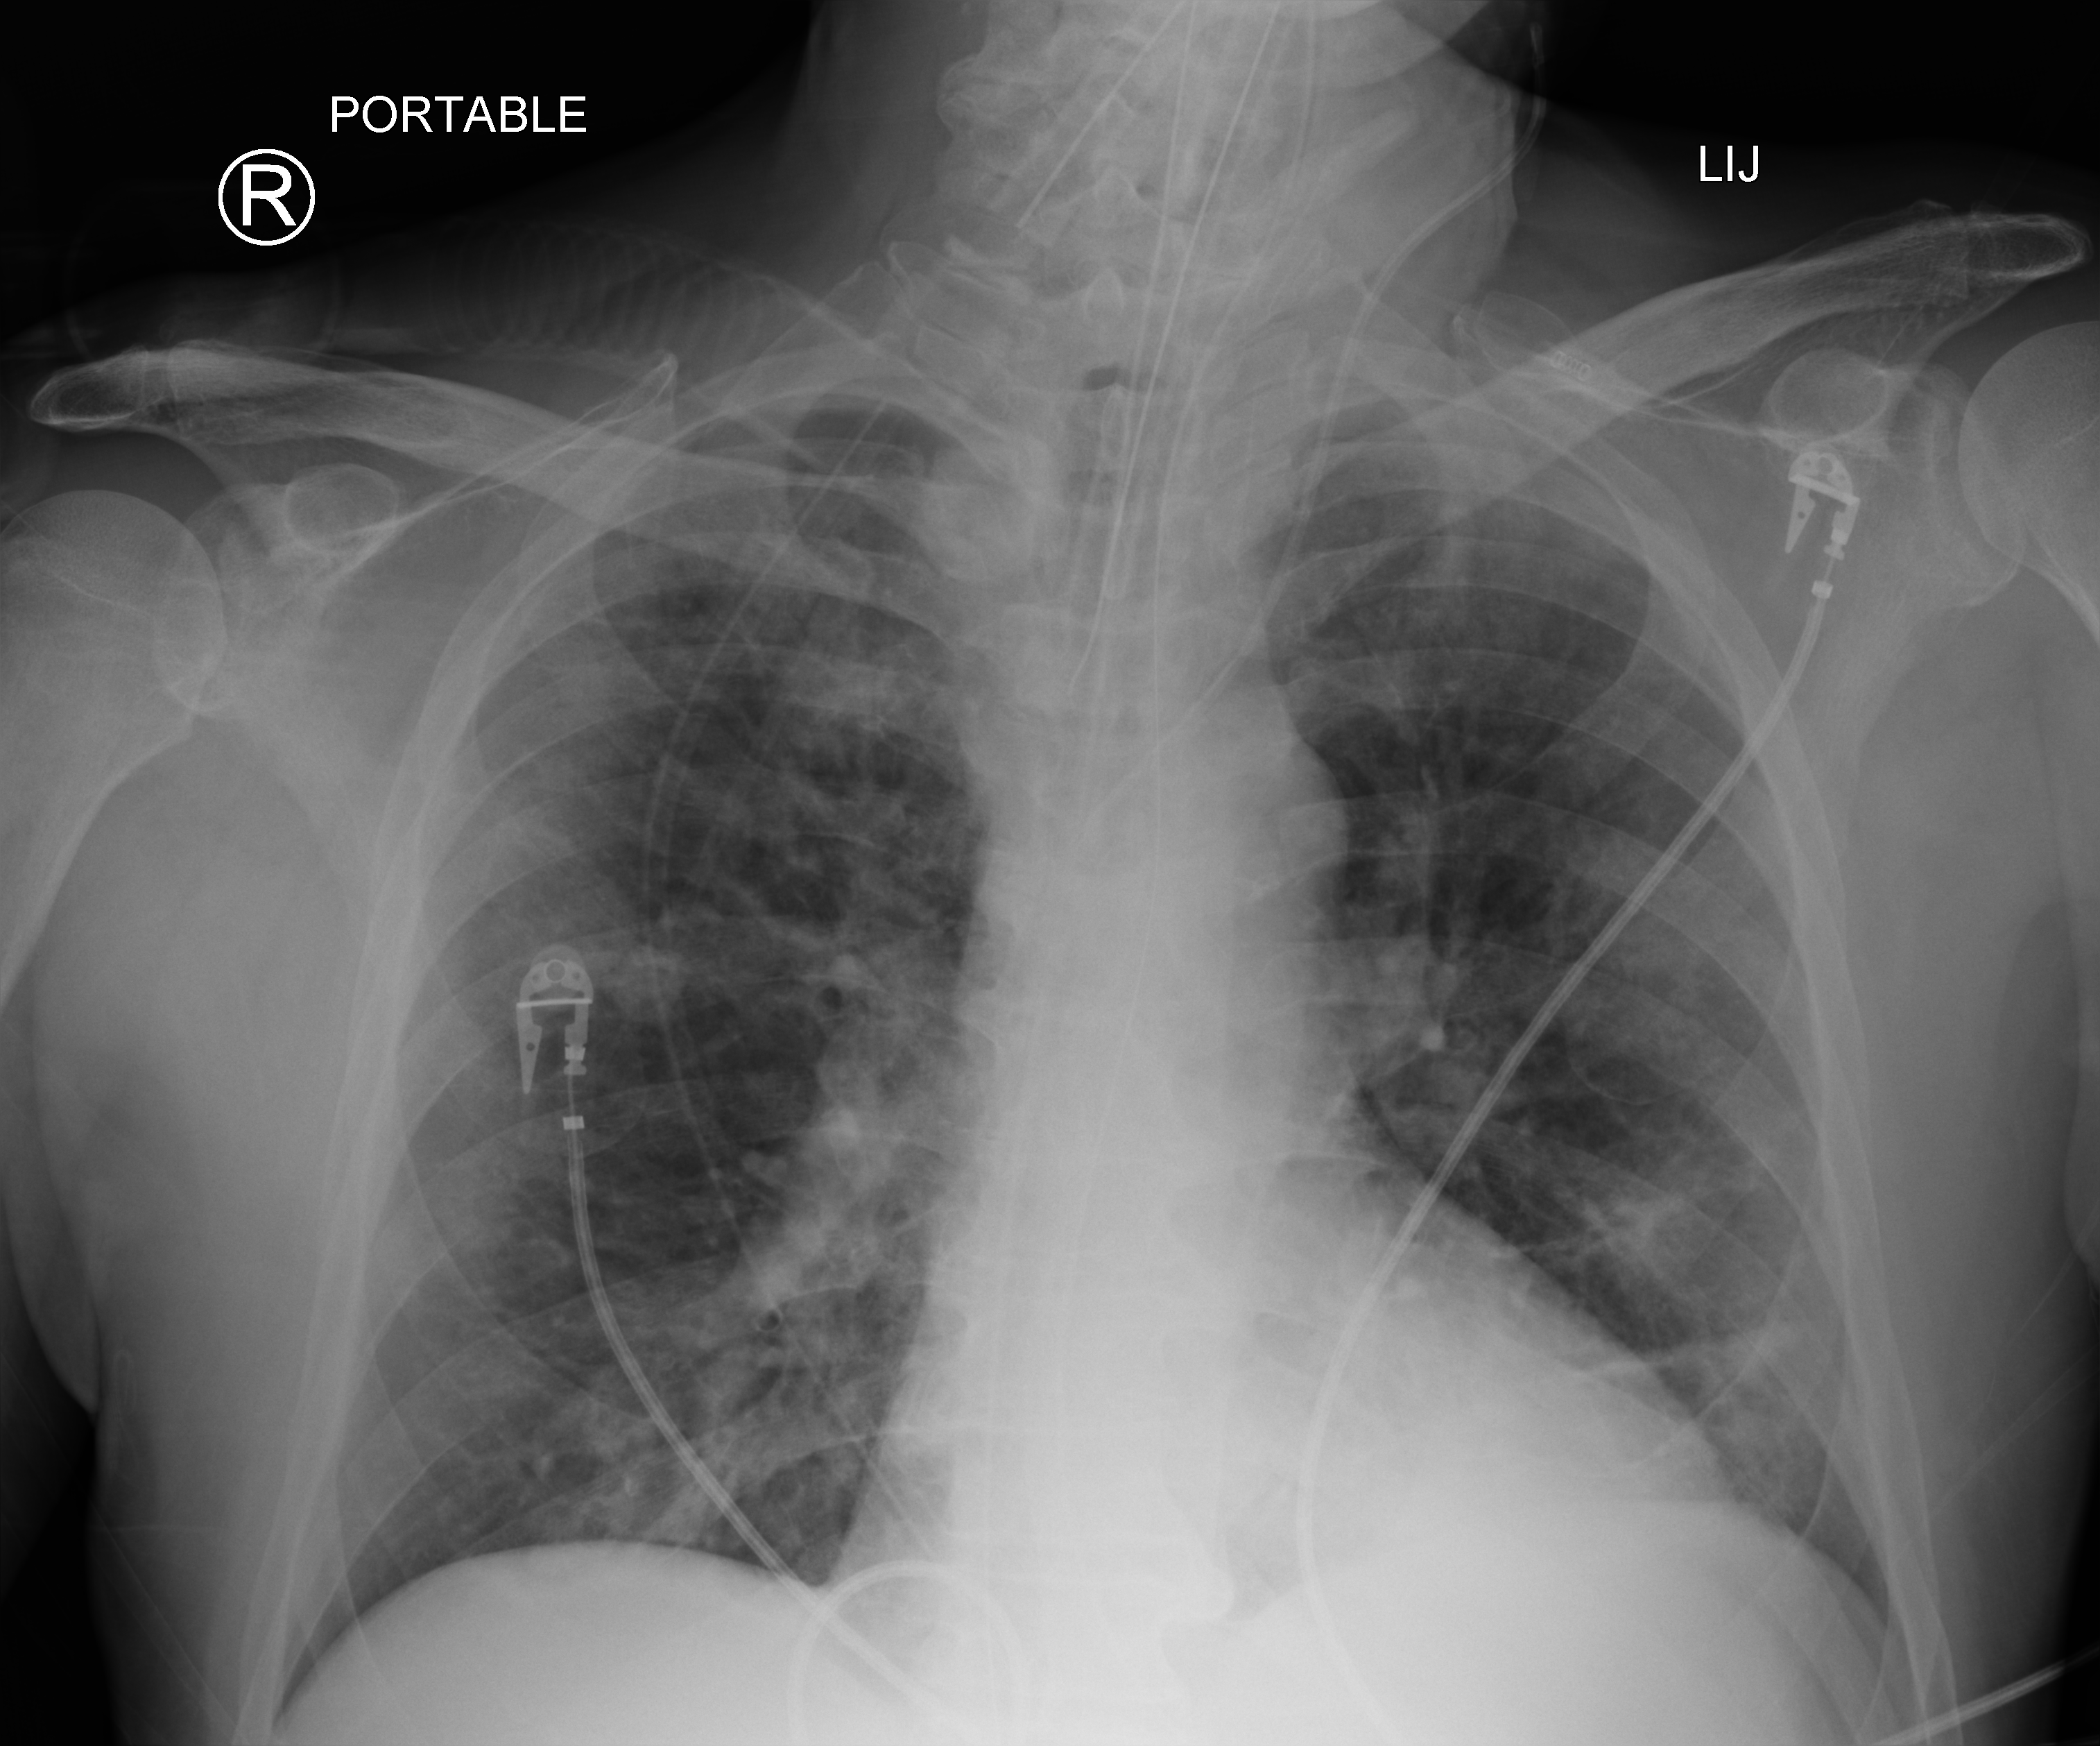
Bedside chest radiograph (computed radiography), anteroposterior (AP) projection. Male patient hospitalised with COVID-19, age 60–74 years.
From the hospital-stay record, not from the radiograph (when in the stay this image was taken is not recorded): smoking status (admission record): never; admitted to intensive care during this hospital stay: yes; mechanically ventilated during this hospital stay: yes.